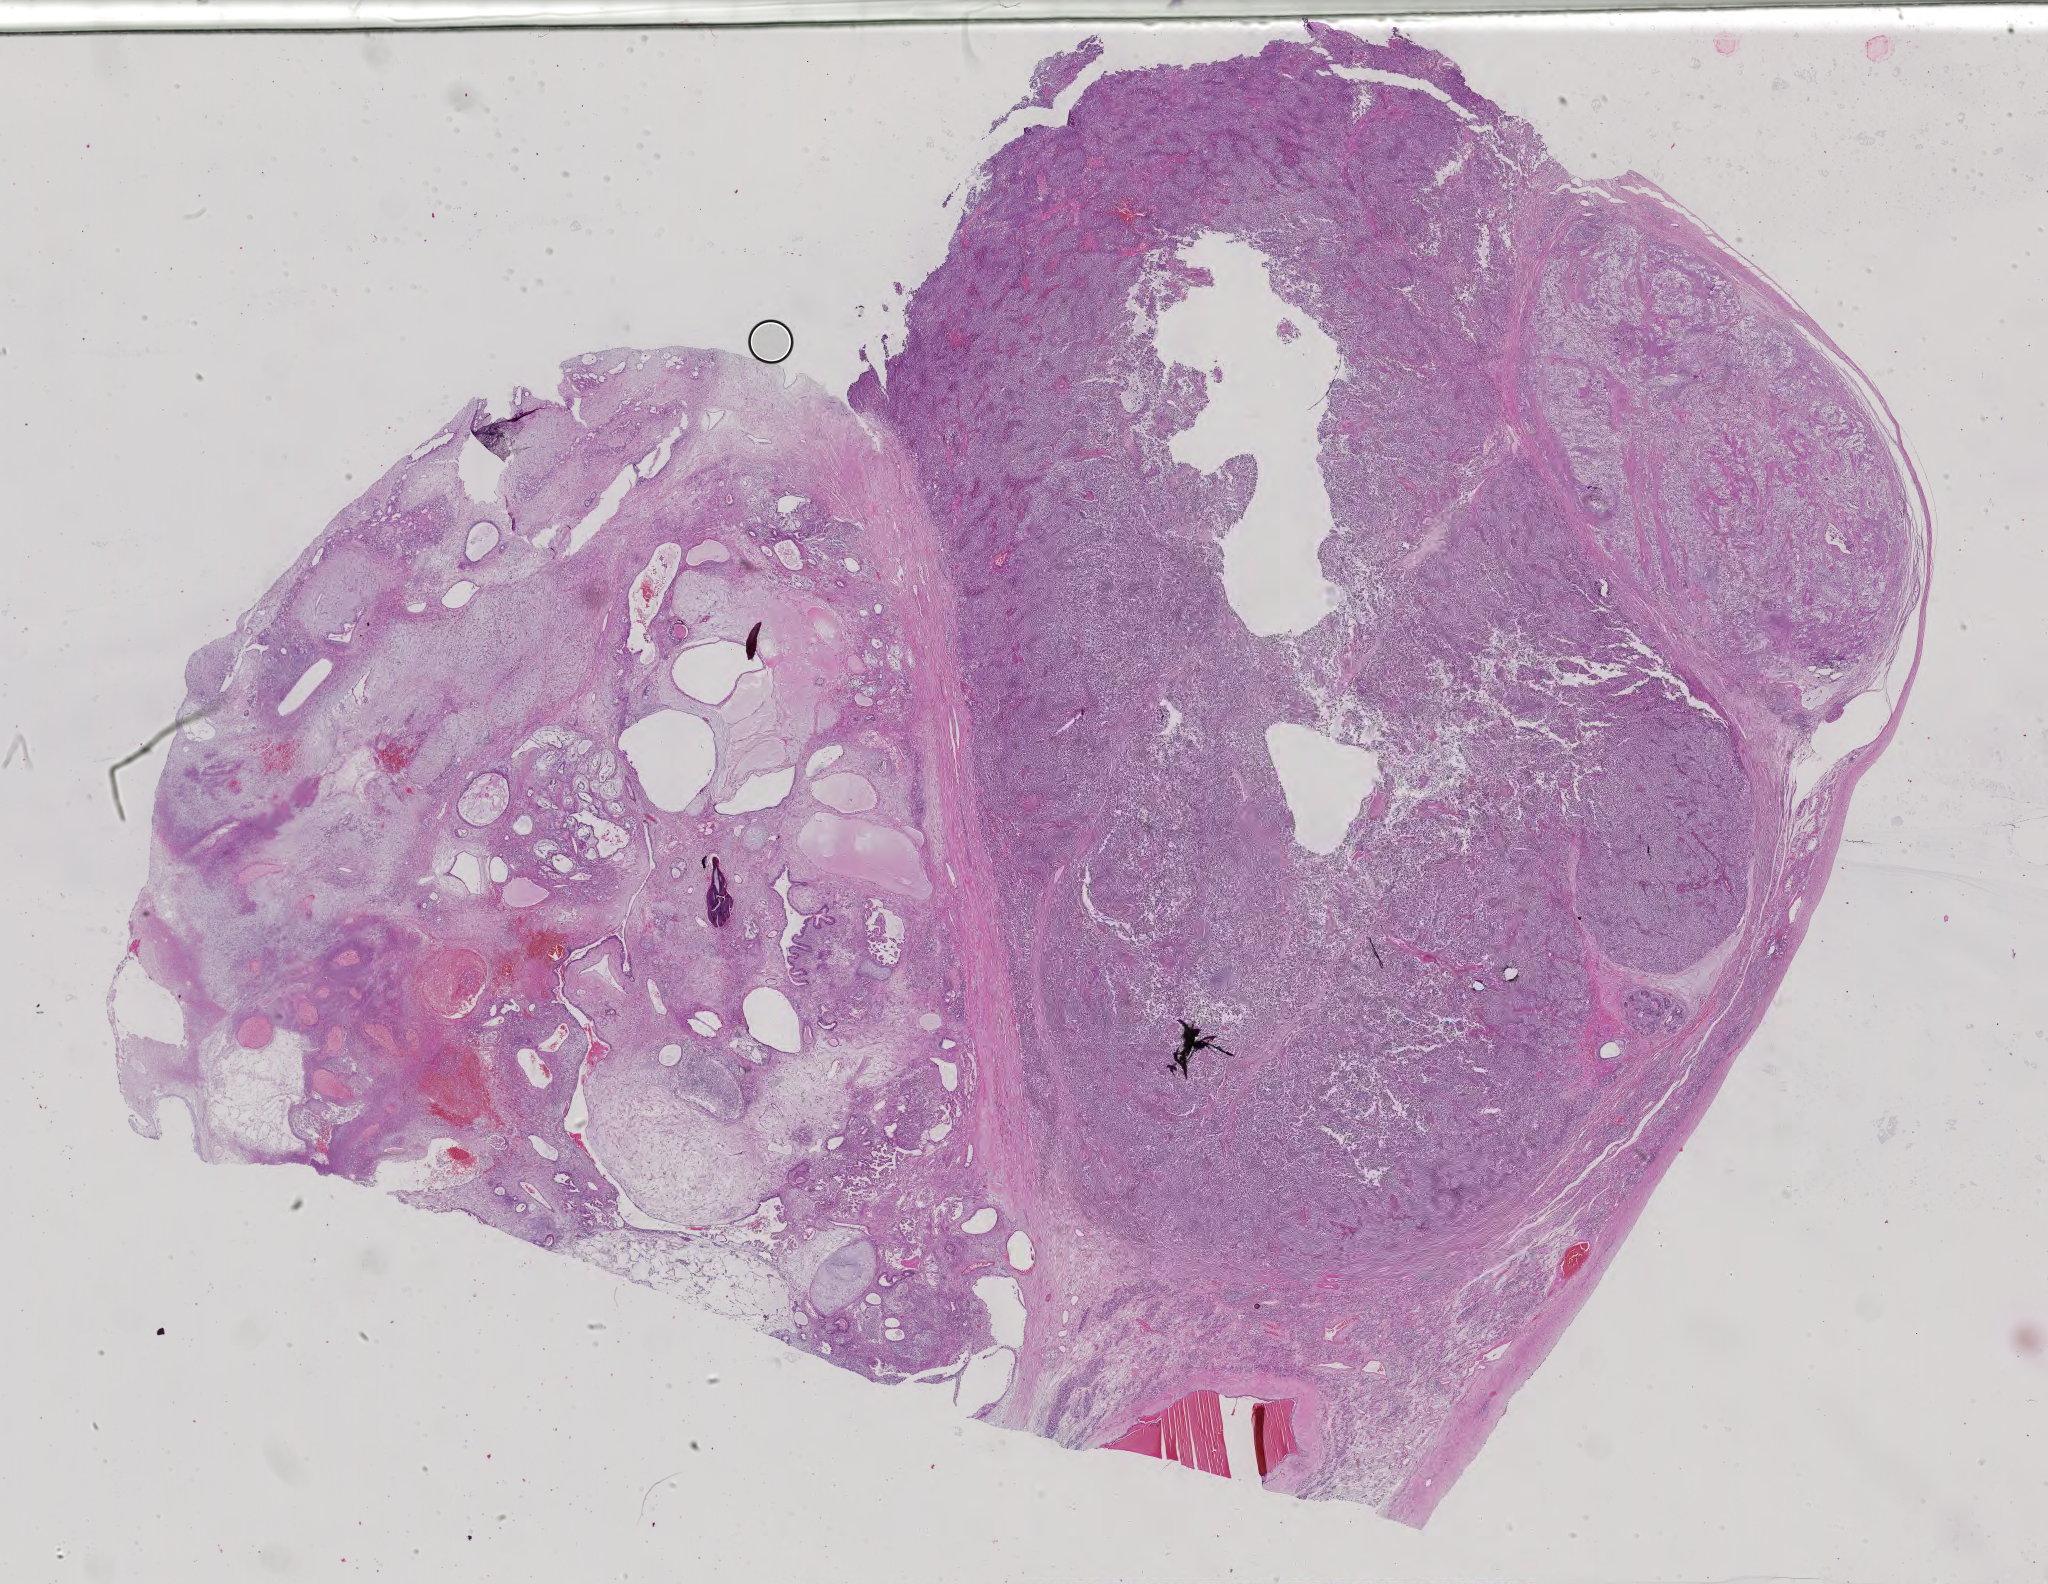
Whole-slide histology image, H&E-stained, a low-resolution overview of the entire scanned area, about 29.8 x 23.1 mm, formalin-fixed paraffin-embedded (FFPE) diagnostic section, testis, primary tumour sample. Male, age 53 years at initial diagnosis.
- AJCC pathologic stage: IS (6th edition)
- pathologic diagnosis: Mixed germ cell tumor